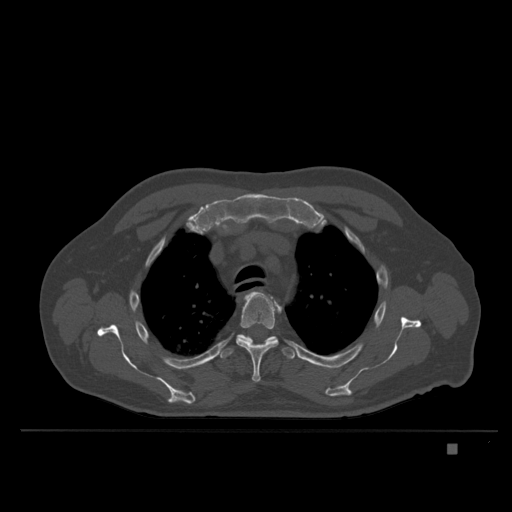
CT including the spine, one axial slice. Slice 285 of 435 in the series (ordered by position). Bone window (W 1800 / L 400 HU). 1.5 mm slice thickness. 512 × 512 image matrix, field of view 434 × 434 mm. Male patient, age 73 years. From the clinical record (not read from this slice): primary cancer: skin.
Annotated regions visible in this slice (semi-automatically segmented with operator editing):
- T3 vertebra: bounding box <275,303,280,310> (left, top, right, bottom; pixels)
- T4 vertebra: <236,291,282,383>
- T5 vertebra: <221,334,294,360>